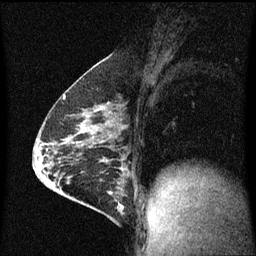
Breast MRI (dynamic contrast-enhanced), one sagittal slice; position 34 of 60 along the scan axis; dynamic contrast-enhanced series, image 2 of 3 at this slice position (ordered by acquisition); 1.5 T; TE 4.2 ms, TR 8 ms; 2 mm slice thickness; 256 × 256 image matrix, field of view 200 × 200 mm. Patient: female, 64 years.
Outlined on this slice (semi-automatically segmented with operator editing):
- analysis volume of interest (the breast-tissue region the enhancement analysis was run in; not a lesion): bounding box <87,176,128,217> (left, top, right, bottom; pixels)
- tumour enhancement mask (voxels above the 70 % enhancement threshold inside the analysis volume of interest): <101,180,123,213>